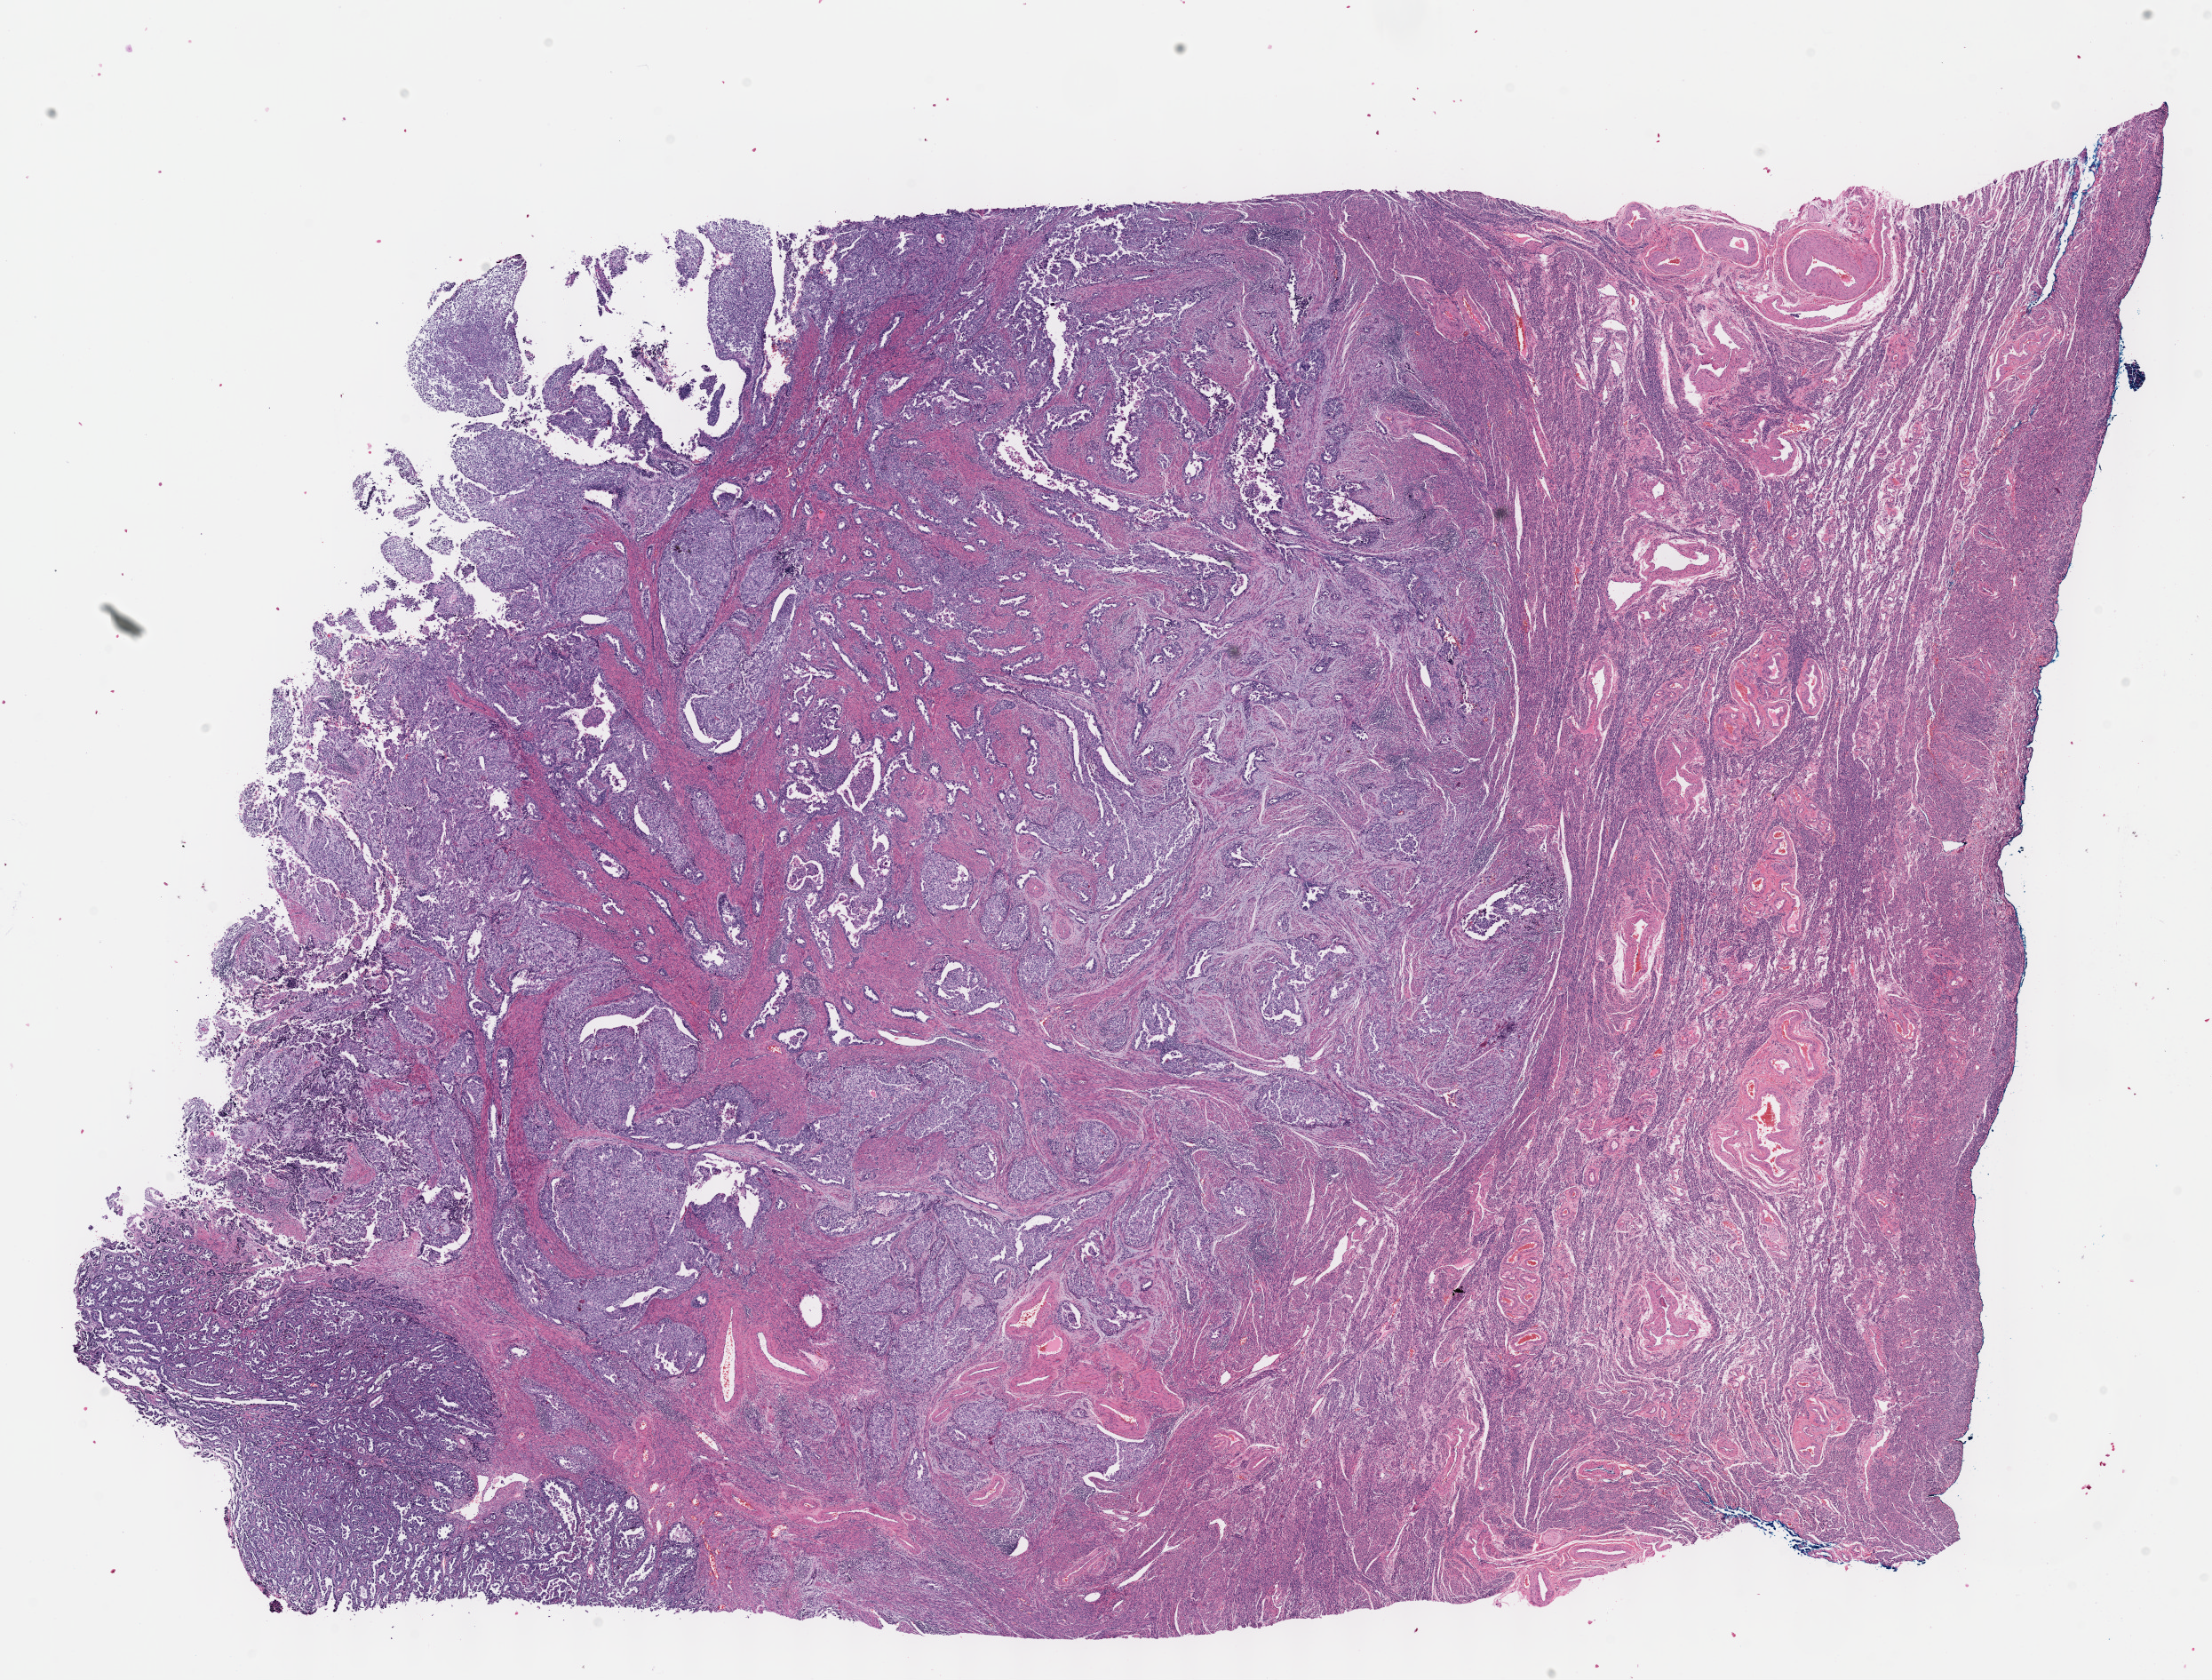
H&E whole-slide image — whole scanned area (about 20.1 x 15.3 mm, acquisition: 40x scan) shown as a low-resolution overview. FFPE section. Primary tumour sample from the uterus. Female patient; age at initial diagnosis 67 years. Histologic grade: G3 (poorly differentiated).
Diagnosis: Serous cystadenocarcinoma, NOS. FIGO stage: IIIC.